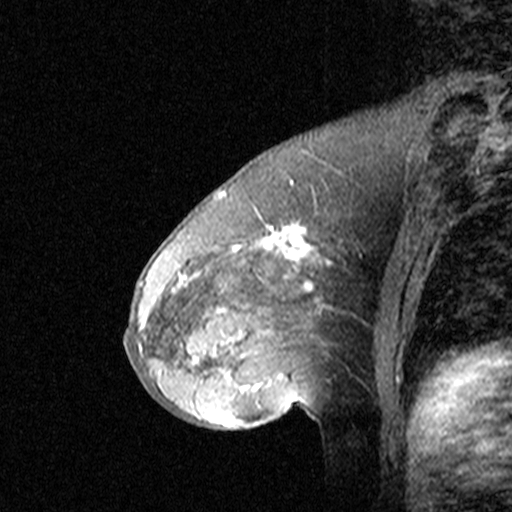
Breast MRI (dynamic contrast-enhanced), one sagittal slice. Position 25 of 44 along the scan axis. Dynamic contrast-enhanced study with each time point stored as its own series, time point 2 of 3 at this slice position (early post-contrast, ordered by acquisition time). 1.5 T. TE 4.5 ms, TR 11 ms. 3 mm slice thickness. 512 × 512 image matrix. Female patient, age 46 years. Case-level facts recorded for this patient, not image findings: setting: breast cancer imaged before/during neoadjuvant chemotherapy; receptor status: HER2-positive.
Structures marked on this image (semi-automatically segmented with operator editing):
- analysis volume of interest (the breast-tissue region the enhancement analysis was run in; not a lesion): bounding box <144,172,359,393> (left, top, right, bottom; pixels)
- tumour enhancement mask (voxels above the 90 % enhancement threshold inside the analysis volume of interest): <144,223,332,393>